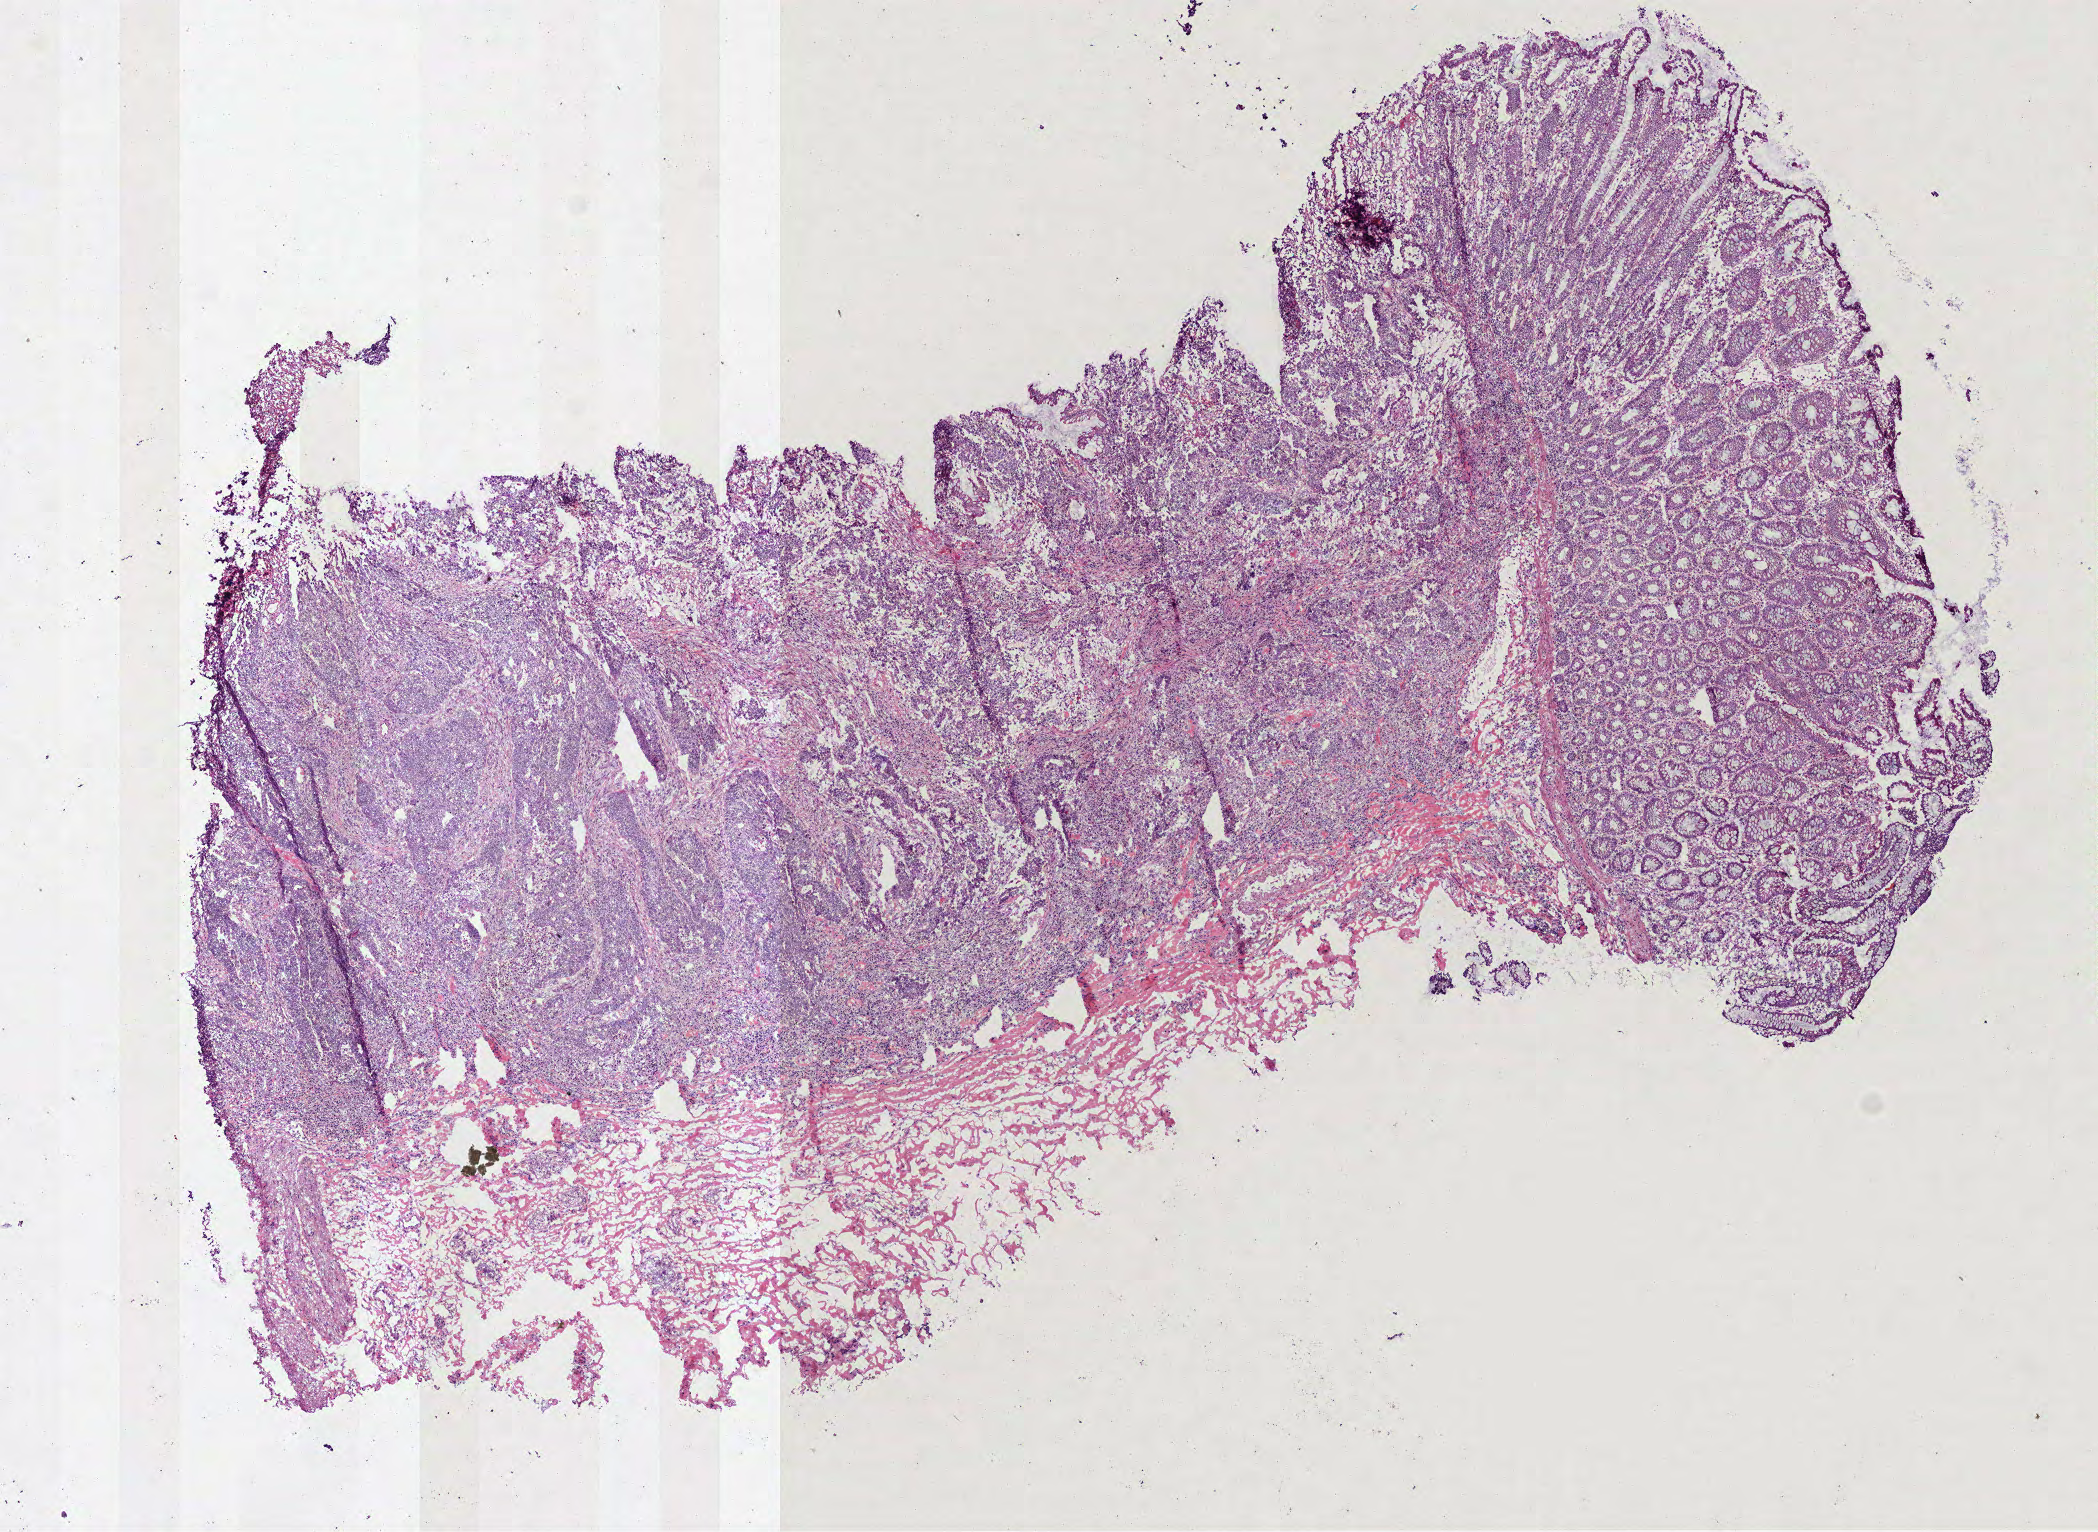
Whole-slide histology image, H&E, a low-resolution overview of the entire scanned area, about 8.5 x 6.2 mm; frozen section; colon, primary tumour sample. Patient: female, age at initial diagnosis 81 years.
Pathologic diagnosis: Adenocarcinoma, NOS.